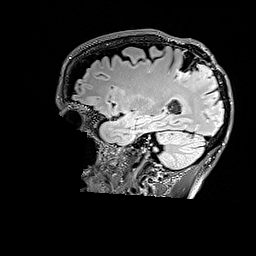
Brain MRI from a brain-tumour surgery series, one sagittal slice. Slice 118 of 176 in the series (ordered by position). T2 FLAIR. 1 mm slice thickness. 256 × 256 image matrix, field of view 256 × 256 mm. From the clinical record (not read from this slice): histopathology: Astrocytoma; WHO grade: 3.
Outlined on this slice (expert manual segmentation):
- tumour: box from (x=176, y=64) to (x=212, y=80) px
- tumour: (x=201, y=67)–(x=212, y=81)